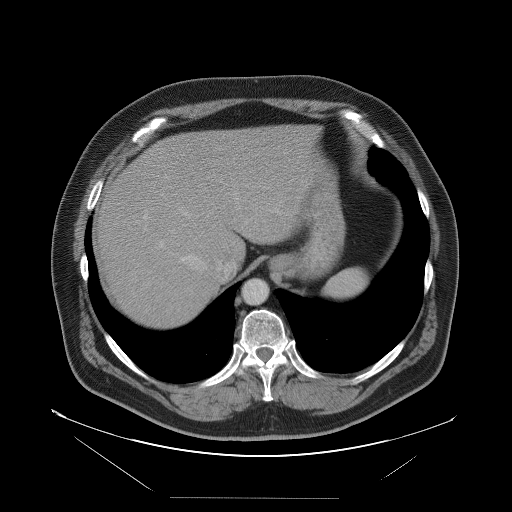
Contrast-enhanced abdominal CT, one axial slice; slice 80 of 114 in the series (ordered by position); soft-tissue window (W 400 / L 40 HU); 5 mm slice thickness; 512 × 512 image matrix, field of view 500 × 500 mm. Male patient, age 61 years. From the clinical record (not read from this slice): diagnosis: colorectal cancer liver metastases, imaged before liver resection; multiple liver metastases: no; largest metastasis: 6.5 cm.
Annotated regions visible in this slice (outlined manually by an expert reader):
- hepatic veins: bounding box [x1, y1, x2, y2] px = [178, 185, 282, 280]
- liver: [96, 126, 316, 330]
- planned liver remnant (the part of the liver to remain after resection): [147, 126, 315, 265]
- portal vein (with intrahepatic branches): [143, 214, 164, 248]